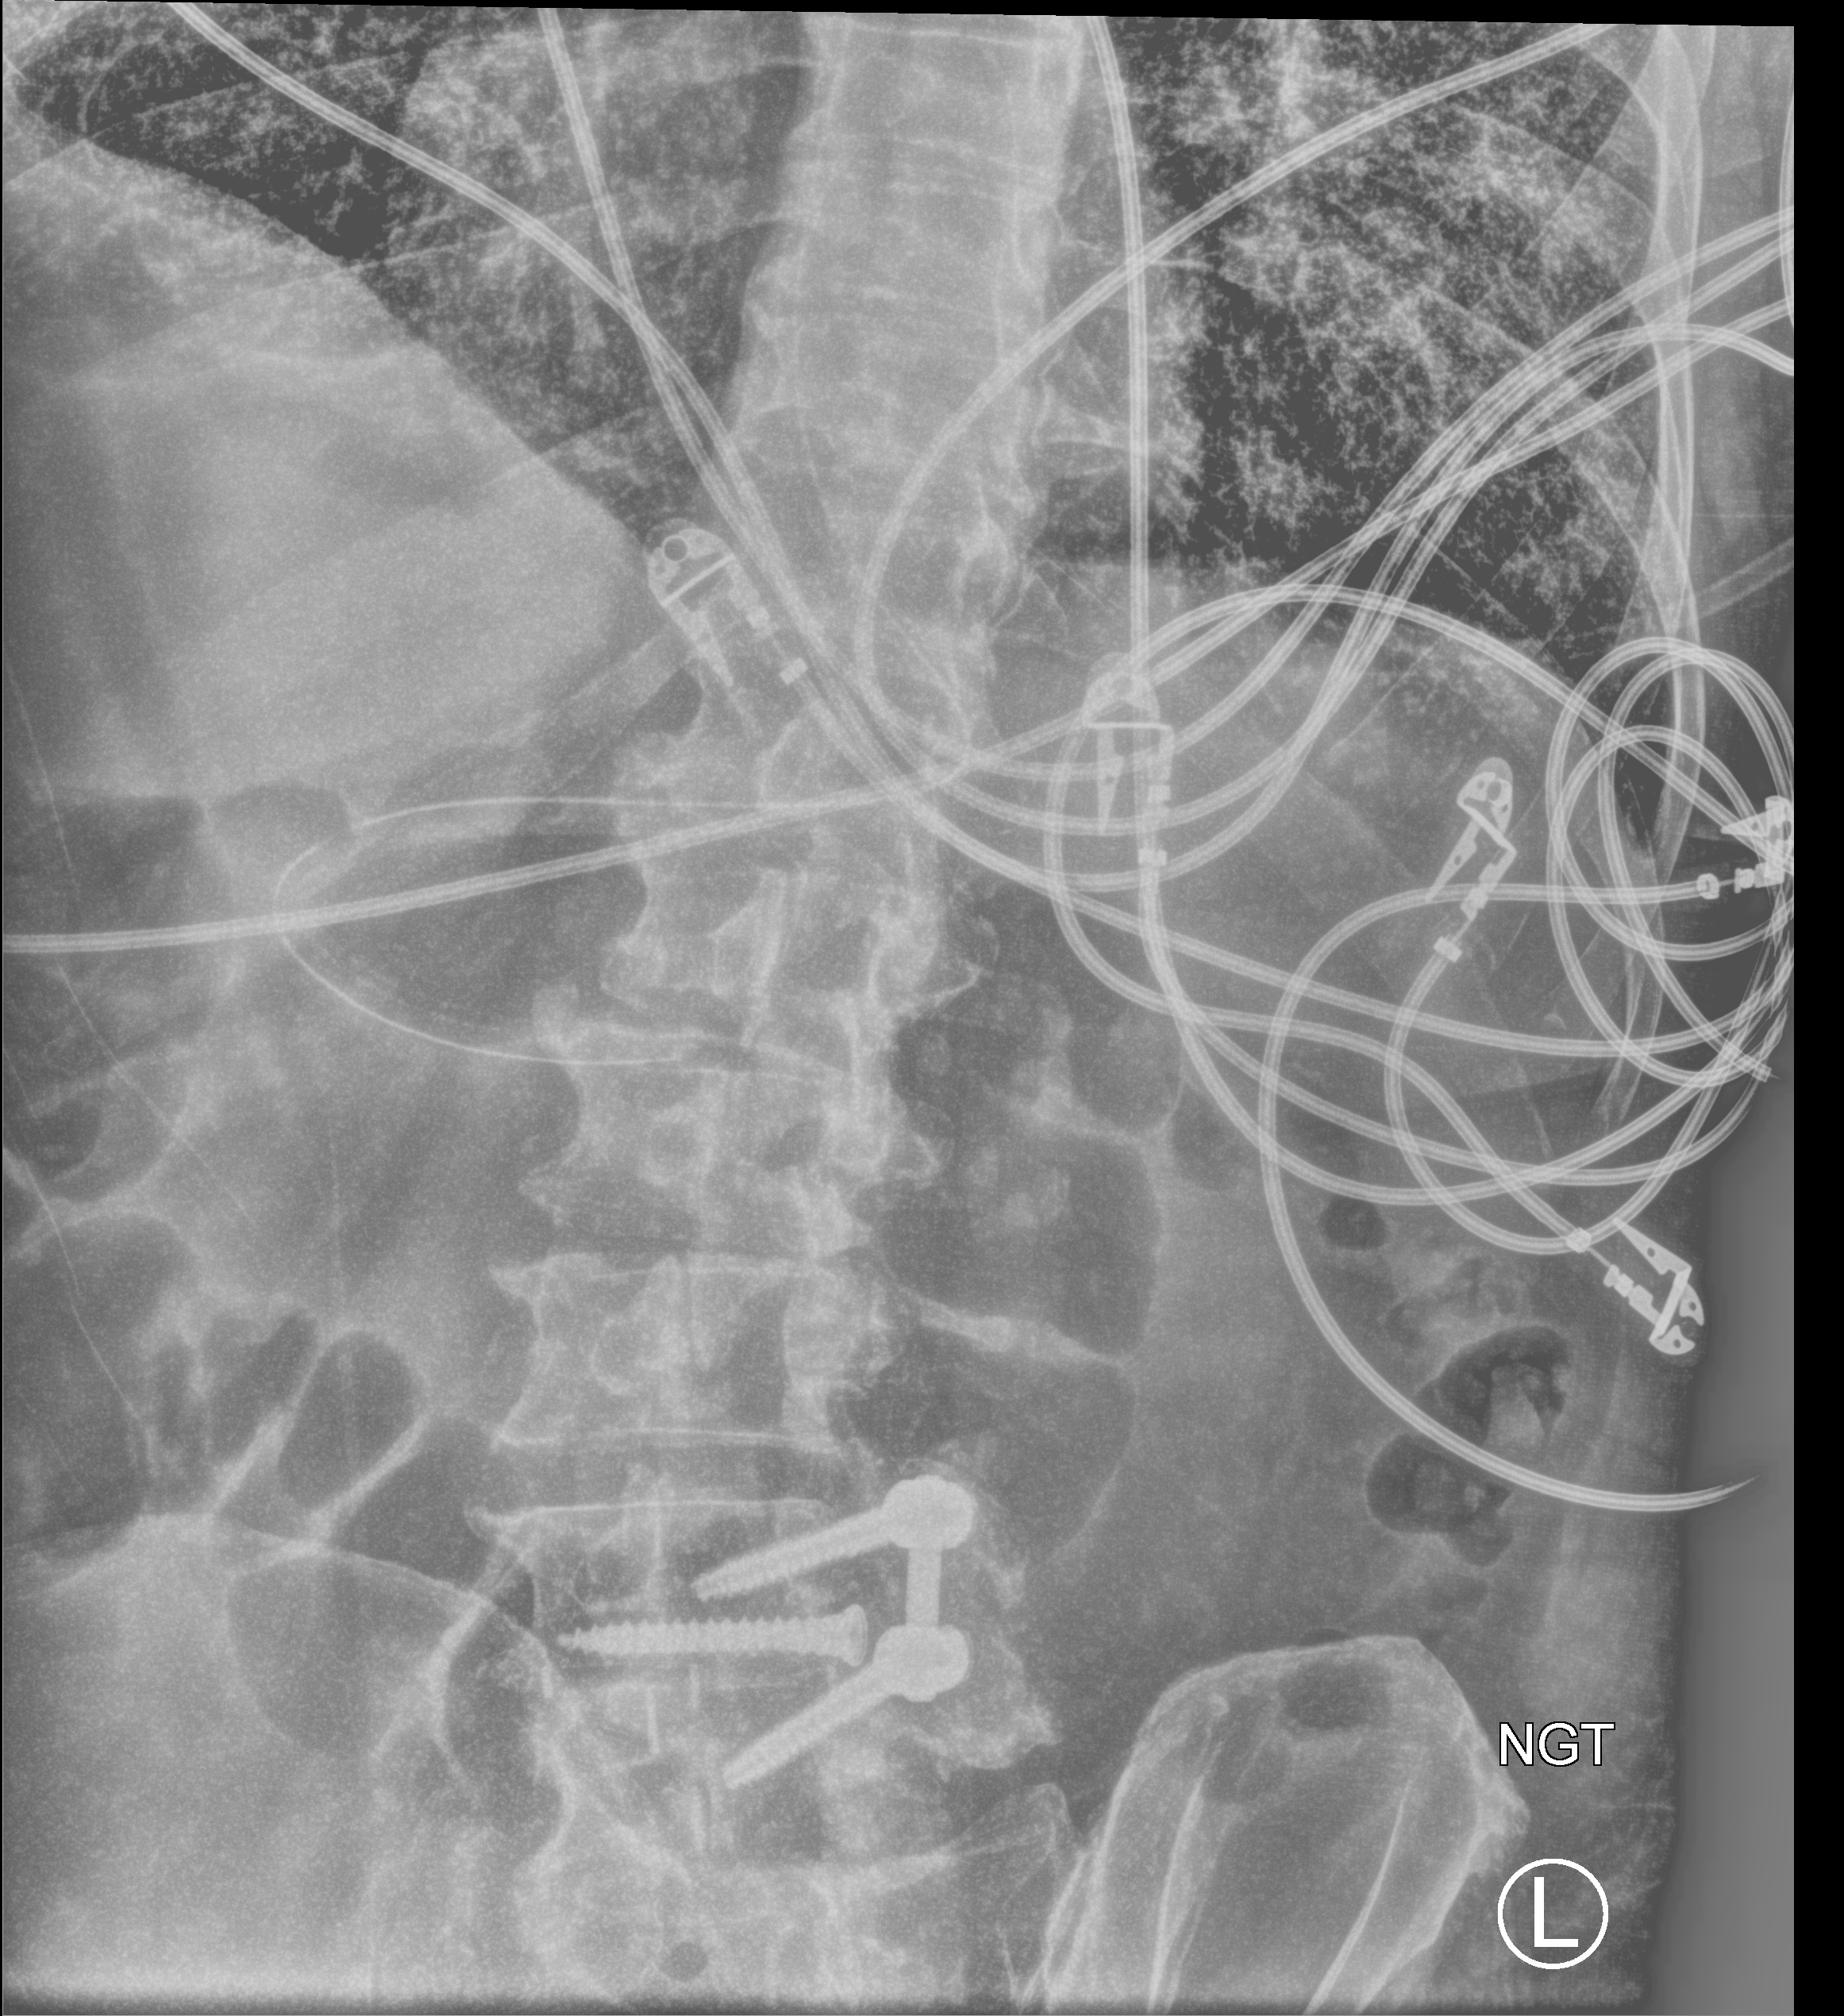
Abdomen X-ray (portable); anteroposterior (AP) projection. Male patient hospitalised with COVID-19, age 60–74 years.
Admission-level facts for this patient (not findings on this image; timing relative to this image not recorded): admitted to intensive care during this hospital stay: yes; mechanically ventilated during this hospital stay: yes.